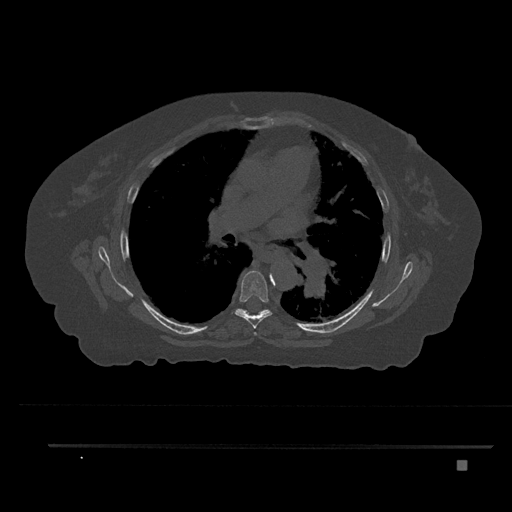
CT including the spine, one axial slice; position 522 of 797 along the scan axis; 120 kVp; bone window (W 1800 / L 400 HU); 0.5 mm slice thickness; 512 × 512 image matrix, field of view 437 × 437 mm. Patient: female, 76 years. Case-level facts recorded for this patient, not image findings: primary cancer: lung; vertebrae with lytic lesions (as recorded): T11, L3.
Structures marked on this image (semi-automatic segmentation, software-assisted and operator-edited):
- T5 vertebra: bounding box (x1, y1, x2, y2) in pixels: (254, 332, 257, 335)
- T6 vertebra: (235, 270, 272, 329)
- T7 vertebra: (236, 309, 270, 316)